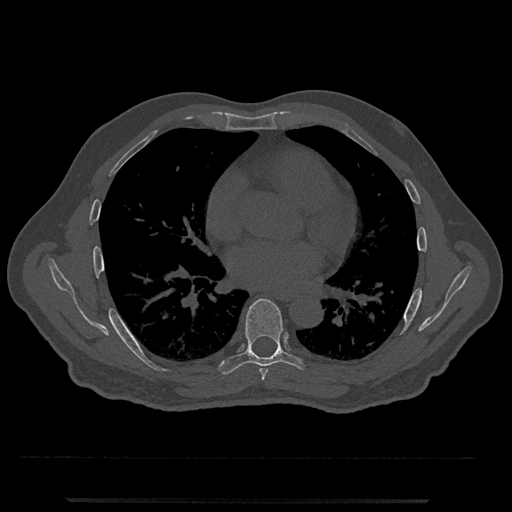
CT including the spine, one axial slice; slice 692 of 797 in the series (ordered by position); reconstruction kernel Br40s/3; bone window (W 1800 / L 400 HU); 0.5 mm slice thickness; 512 × 512 image matrix, field of view 419 × 419 mm. Patient: male, 63 years. Case-level facts recorded for this patient, not image findings: primary cancer: prostate.
Outlined on this slice (semi-automatic segmentation, software-assisted and operator-edited):
- T6 vertebra: bounding box <259,368,268,381> (left, top, right, bottom; pixels)
- T7 vertebra: <218,298,306,375>